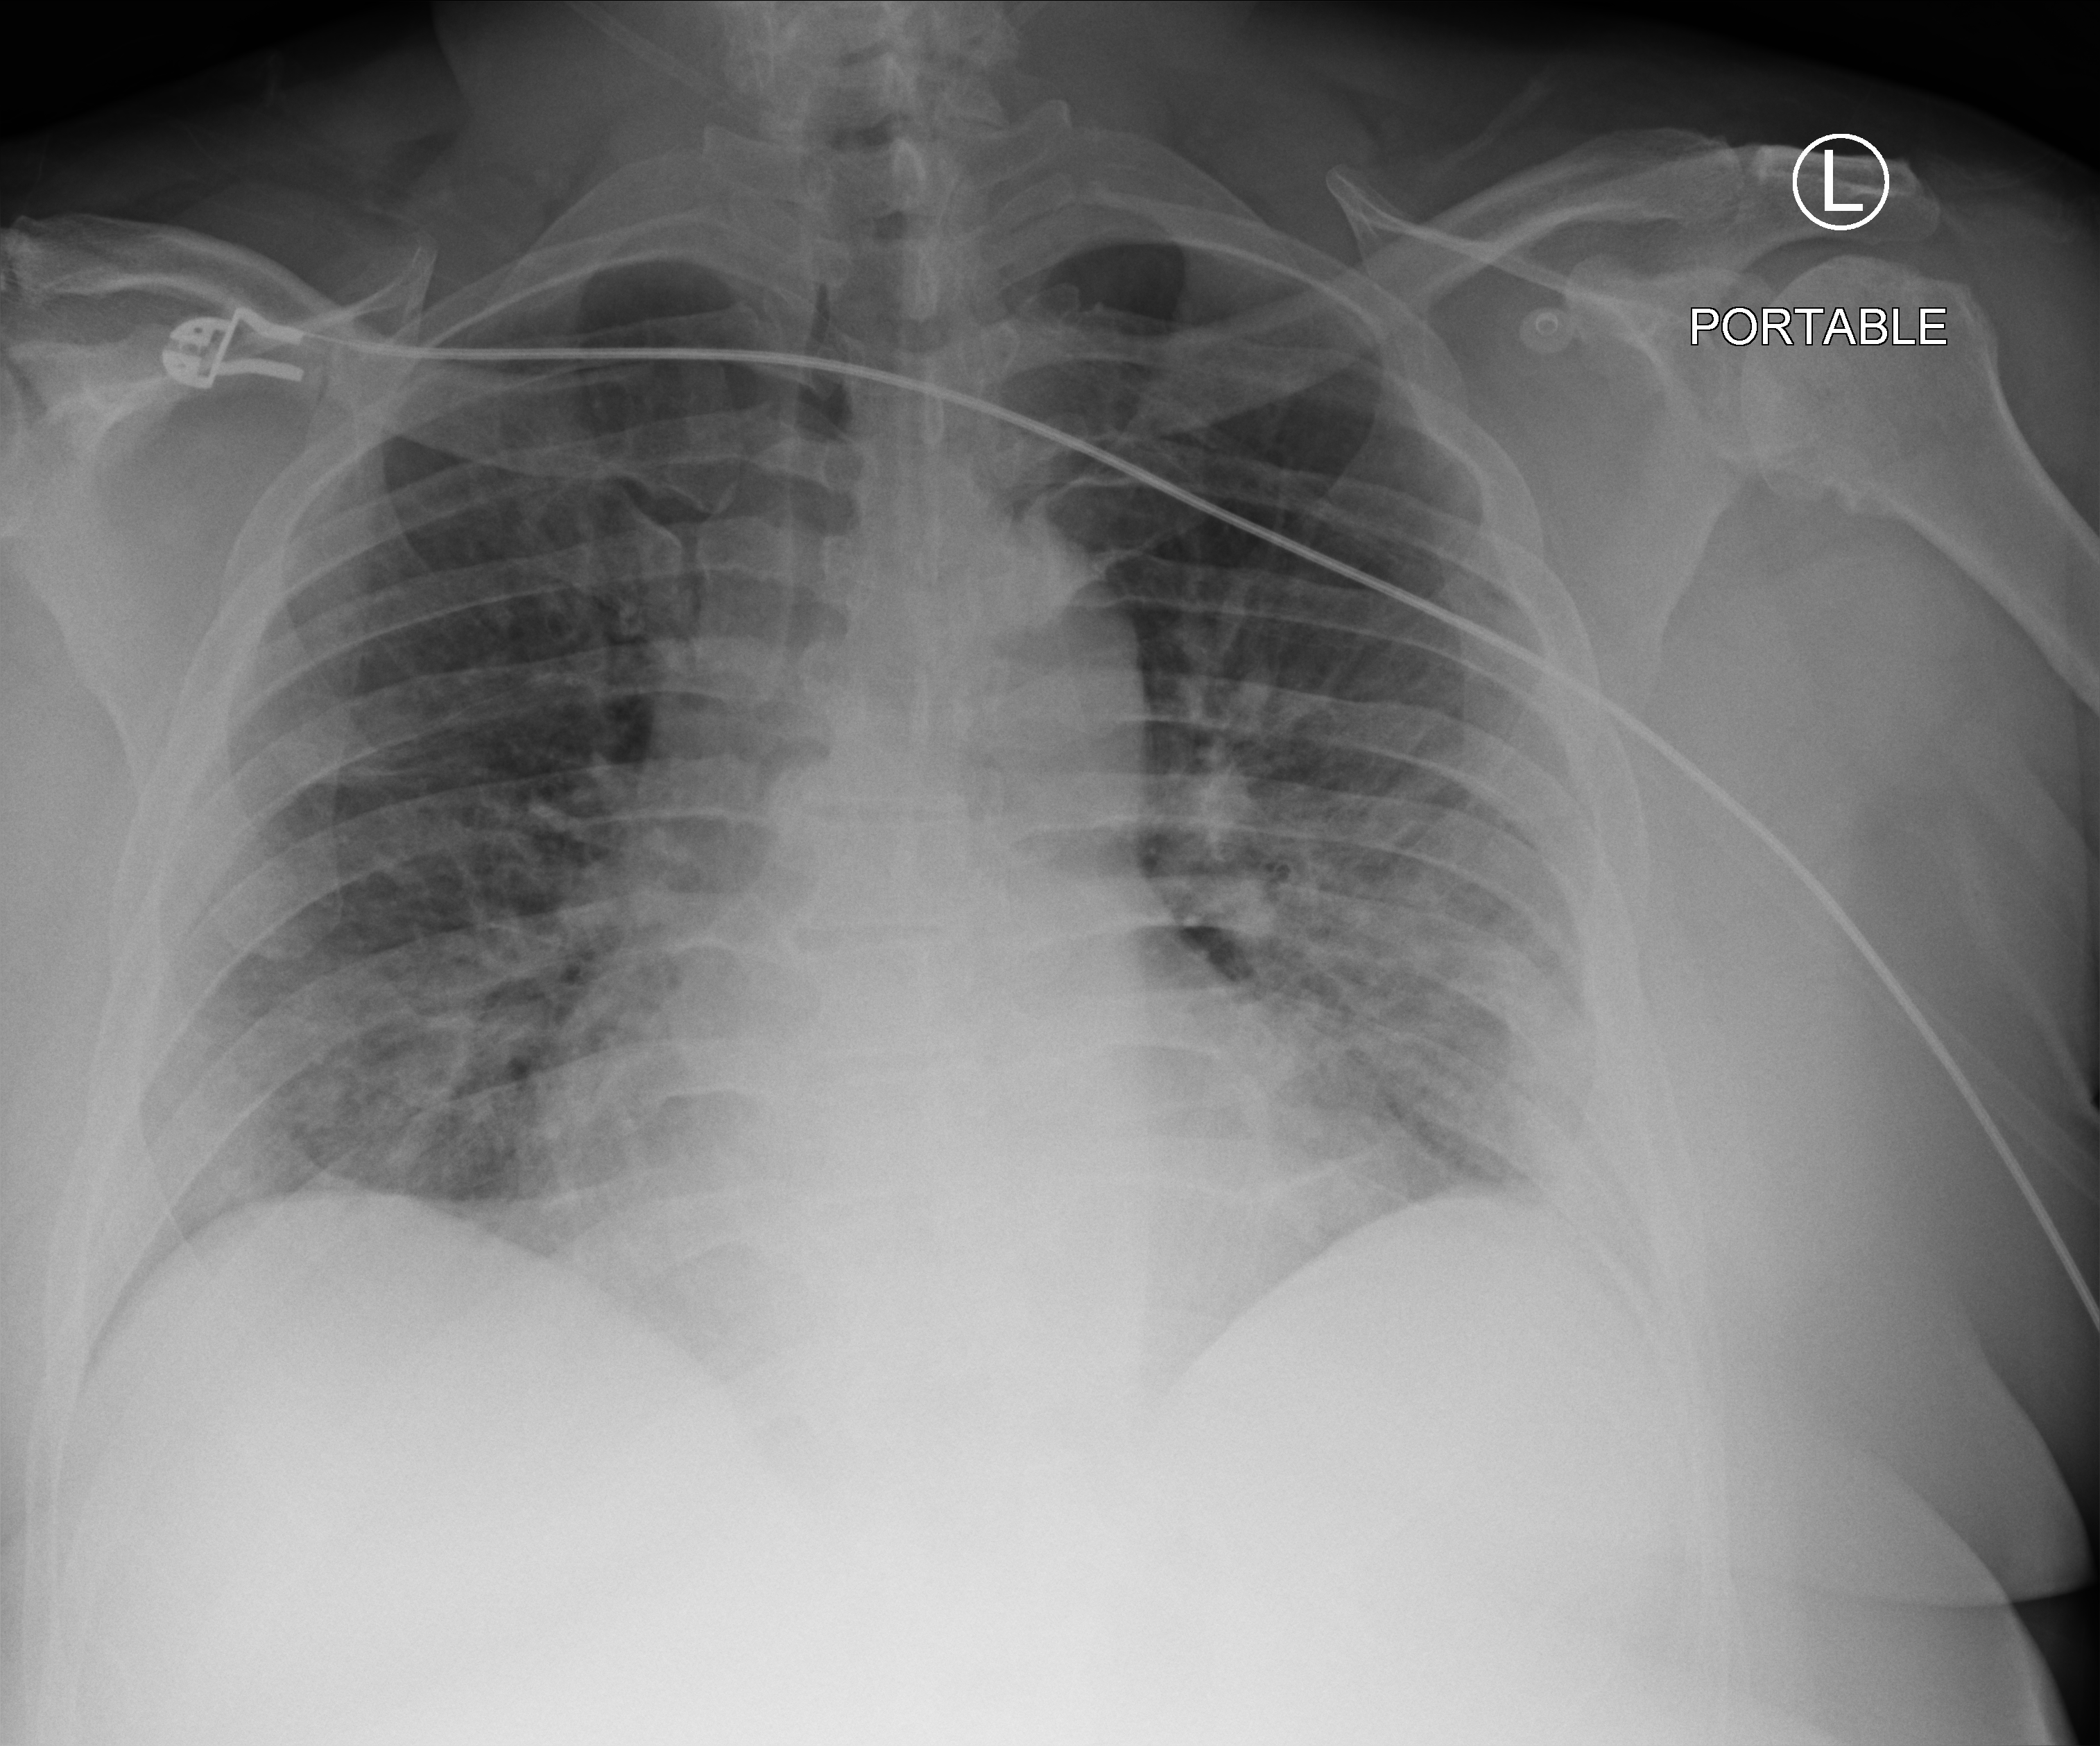
Portable chest radiograph; anteroposterior (AP) projection. Male patient hospitalised with COVID-19, age 18–59 years.
Admission-level facts for this patient (not findings on this image; timing relative to this image not recorded):
- hypertension (admission record): yes